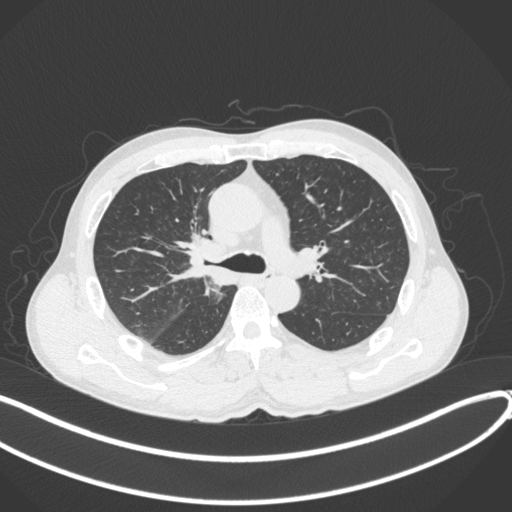
Chest CT, one axial slice; slice 251 of 409 in the series (ordered by position); reconstruction kernel B31f; 120 kVp; lung window (W 1500 / L -600 HU); 1 mm slice thickness; 512 × 512 image matrix, field of view 400 × 400 mm. Male patient, age 53 years. From the clinical record (not read from this slice): clinical TNM (as recorded): T1b N0 M0.
Annotated regions visible in this slice (rectangle marked by the reading radiologist):
- lung tumour (recorded histology: squamous cell carcinoma): bounding box (x1, y1, x2, y2) in pixels: (180, 232, 233, 285)